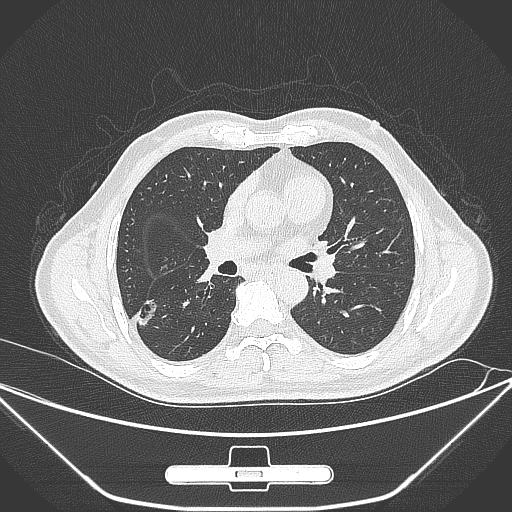
Chest CT, one axial slice. Position 156 of 310 along the scan axis. 120 kVp. Lung window (W 1500 / L -600 HU). 1 mm slice thickness. 512 × 512 image matrix, field of view 398 × 398 mm. Male patient, age 71 years. Case-level facts recorded for this patient, not image findings: clinical TNM (as recorded): T1c N0 M0; histopathological grade: G2.
Outlined on this slice (bounding box drawn by a radiologist):
- lung tumour (recorded histology: adenocarcinoma): box from (x=131, y=292) to (x=163, y=330) px